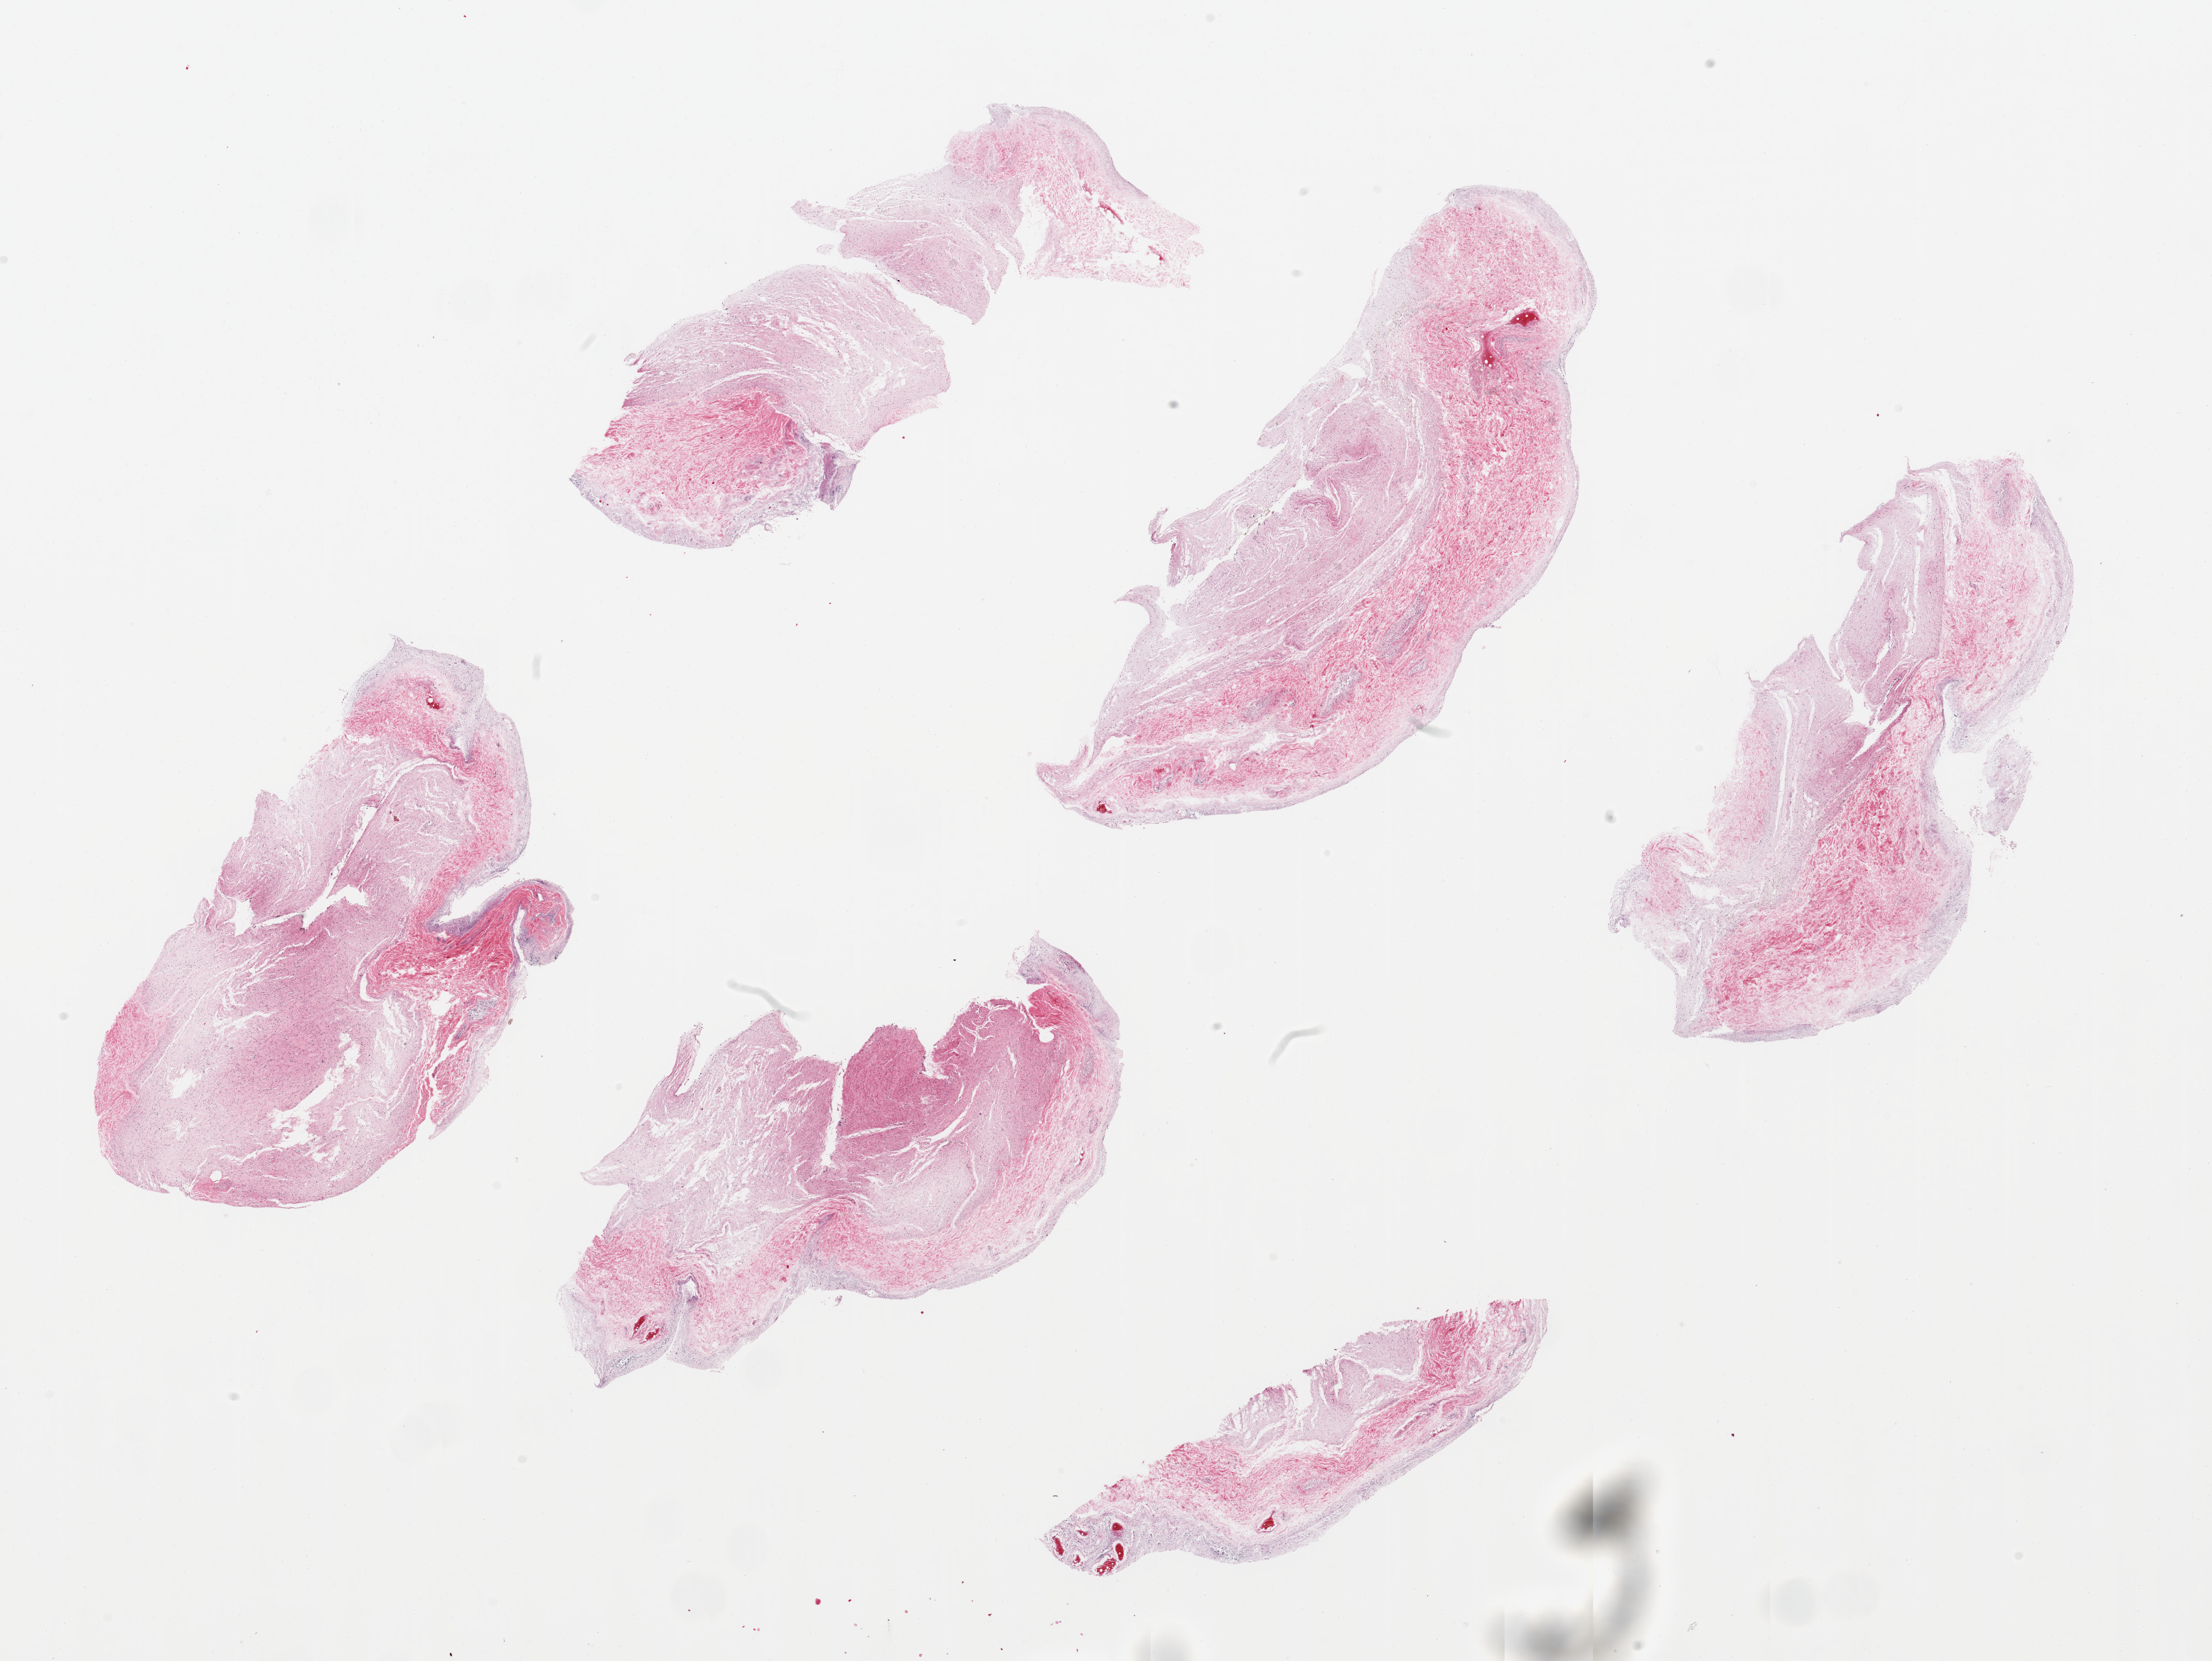
Whole-slide image, haematoxylin and eosin stain, brightfield — a low-resolution overview of the entire scanned area, about 24.6 x 18.5 mm, PAXgene-fixed paraffin-embedded (PFPE) section, section of stomach (target tissue), tissue donor sample. Male donor.
- reviewer comment on this tissue sample: 6 pieces ~7x3mm. Mucosa completely autolyzed/sloughed